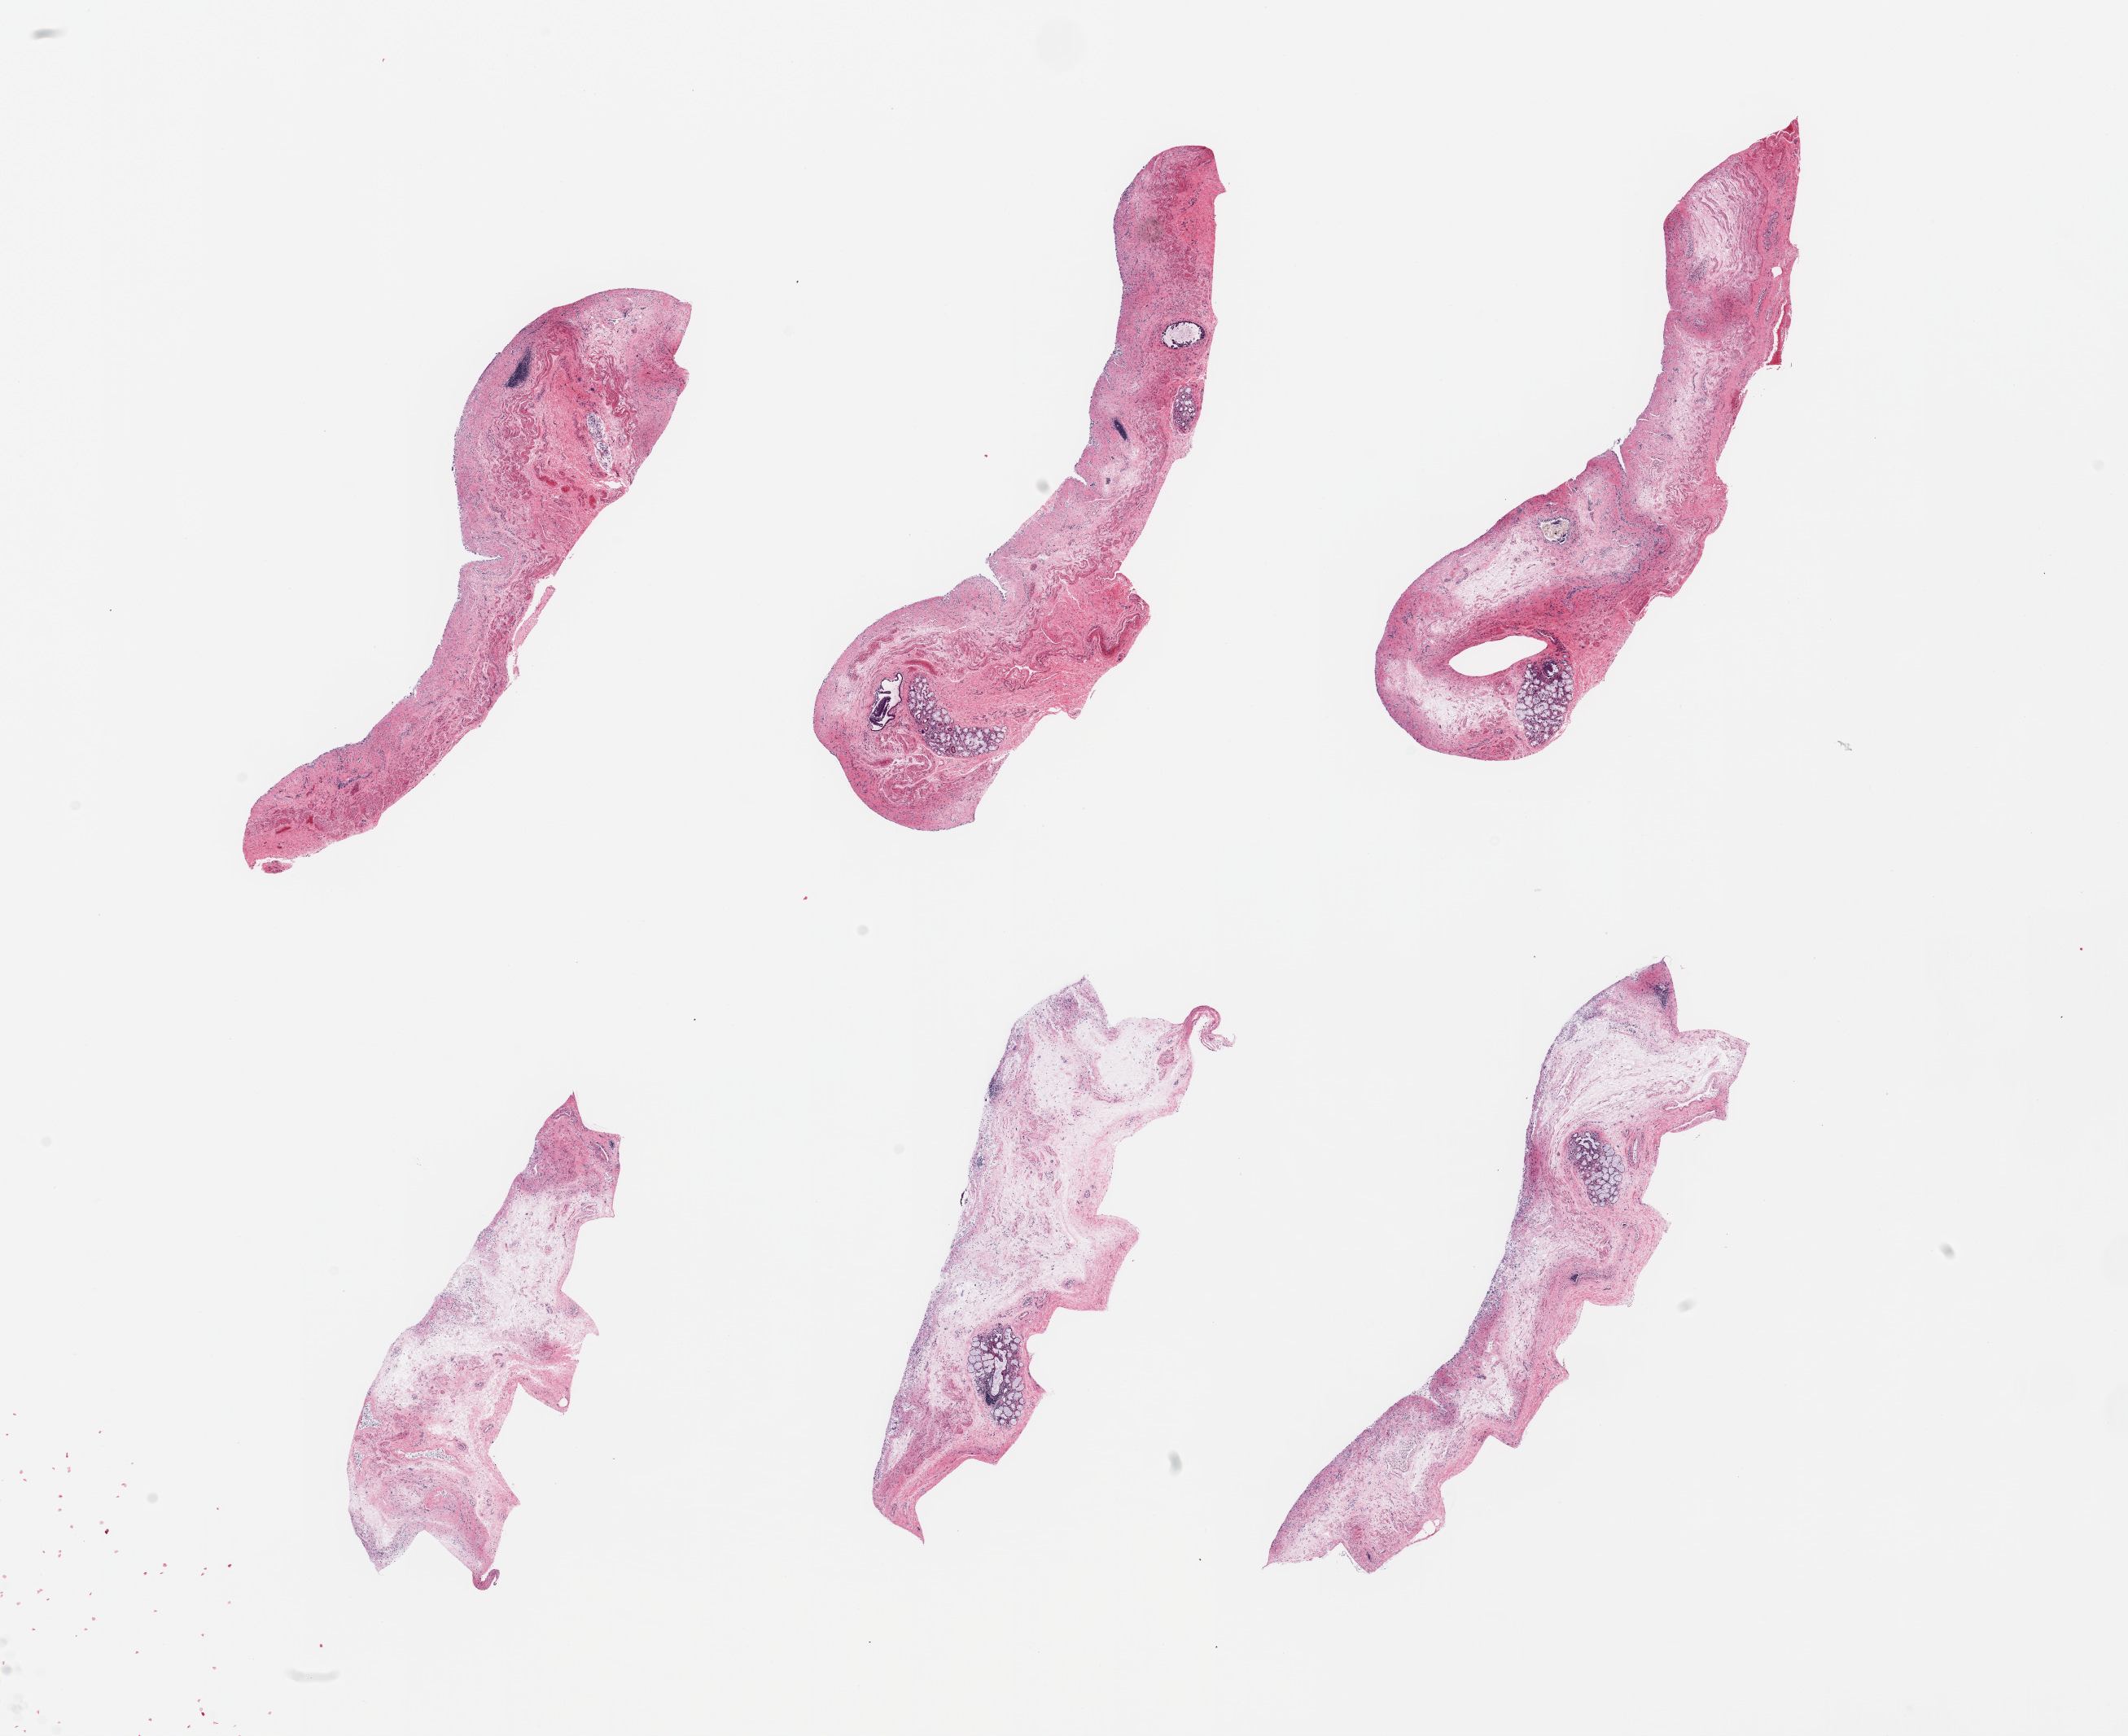
Whole-slide image, hematoxylin and eosin (H&E) stain, brightfield, a low-resolution overview of the entire scanned area, about 20.7 x 16.9 mm (acquisition: 20x scan); PAXgene-fixed, paraffin-embedded tissue; section of esophageal mucous membrane (target tissue); tissue donor sample. Donor sex: male.
Pathologist's review note for this sample: 6 pieces; epithelium totally sloughed; remainder consists mainly of submucosa.